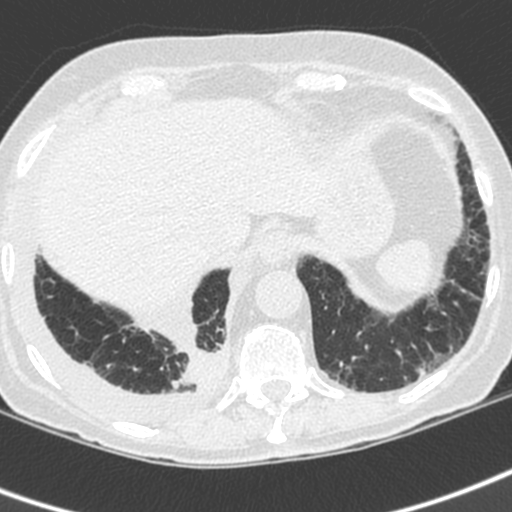
Axial slice from a low-dose chest CT screening exam; first (baseline) screen; lung window (W 1500 / L -600 HU); 1.3 mm slice thickness; 512 × 512 image matrix. Female, age 73 years at enrolment. Current smoker at enrolment.
Expert-annotated lung lesion, bounding box (x1, y1, x2, y2) in pixels: (161, 328, 235, 406). Reader record for this screening exam (exam-level; its link to the box is not recorded): non-calcified nodule or mass ≥4 mm, right lower lobe, 35 × 30 mm, spiculated (stellate) margins, soft tissue attenuation. Later outcome: lung cancer diagnosed 22 days after this screen — adenocarcinoma, NOS, right lower lobe, stage IV (AJCC 6th edition), 35 mm at pathology.